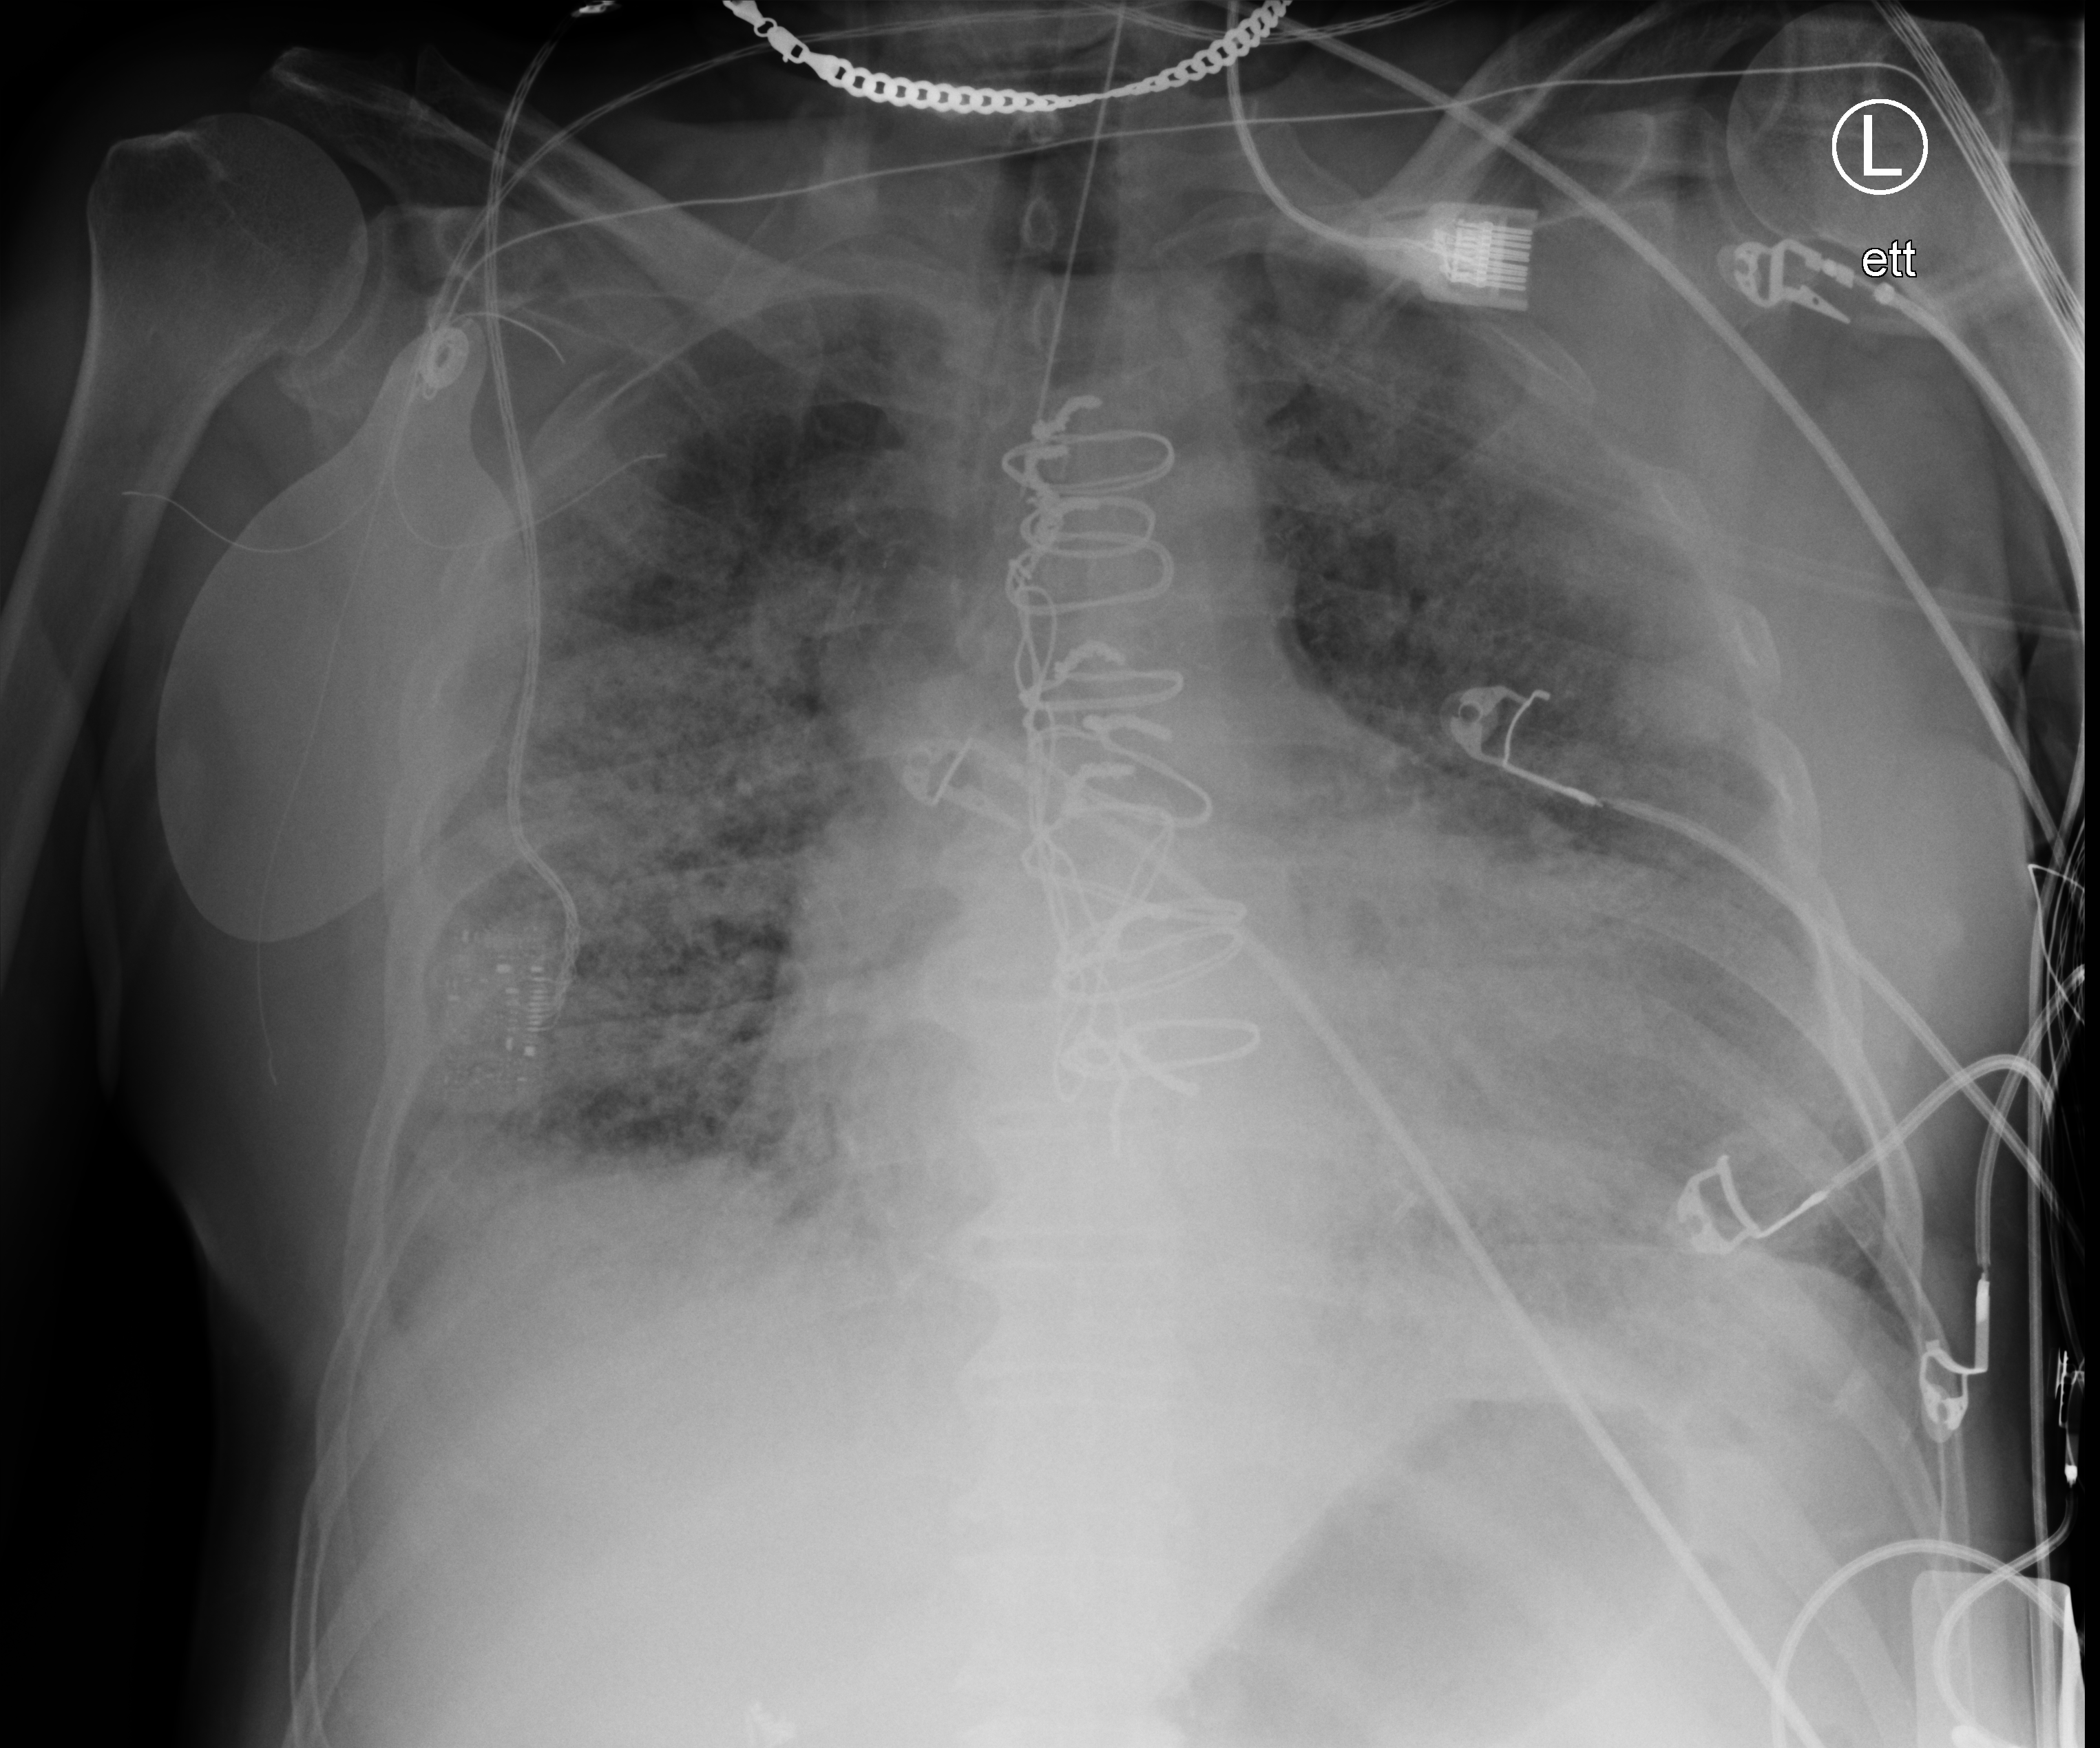
Bedside chest radiograph (computed radiography), anteroposterior (AP) projection. Patient hospitalised with COVID-19; male, aged 75–90 years.
Hospital-stay facts (about this admission, not read from this image; timing relative to this image not recorded):
- mechanically ventilated during this hospital stay: yes